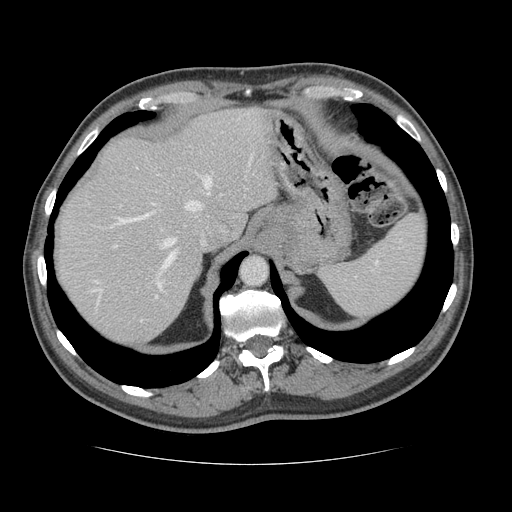
Contrast-enhanced abdominal CT, one axial slice; position 102 of 134 along the scan axis; 120 kVp; intravenous contrast given; soft-tissue window (W 400 / L 40 HU); 512 × 512 image matrix, field of view 377 × 377 mm. Male patient, age 68 years. Case-level facts recorded for this patient, not image findings: diagnosis: colorectal cancer liver metastases, imaged before liver resection; multiple liver metastases: yes; largest metastasis: 2.2 cm; disease in both lobes: no.
Annotated regions visible in this slice (outlined manually by an expert reader):
- hepatic veins: bounding box <92,154,253,292> (left, top, right, bottom; pixels)
- liver: <55,108,276,348>
- planned liver remnant (the part of the liver to remain after resection): <54,108,276,323>
- portal vein (with intrahepatic branches): <114,245,157,298>